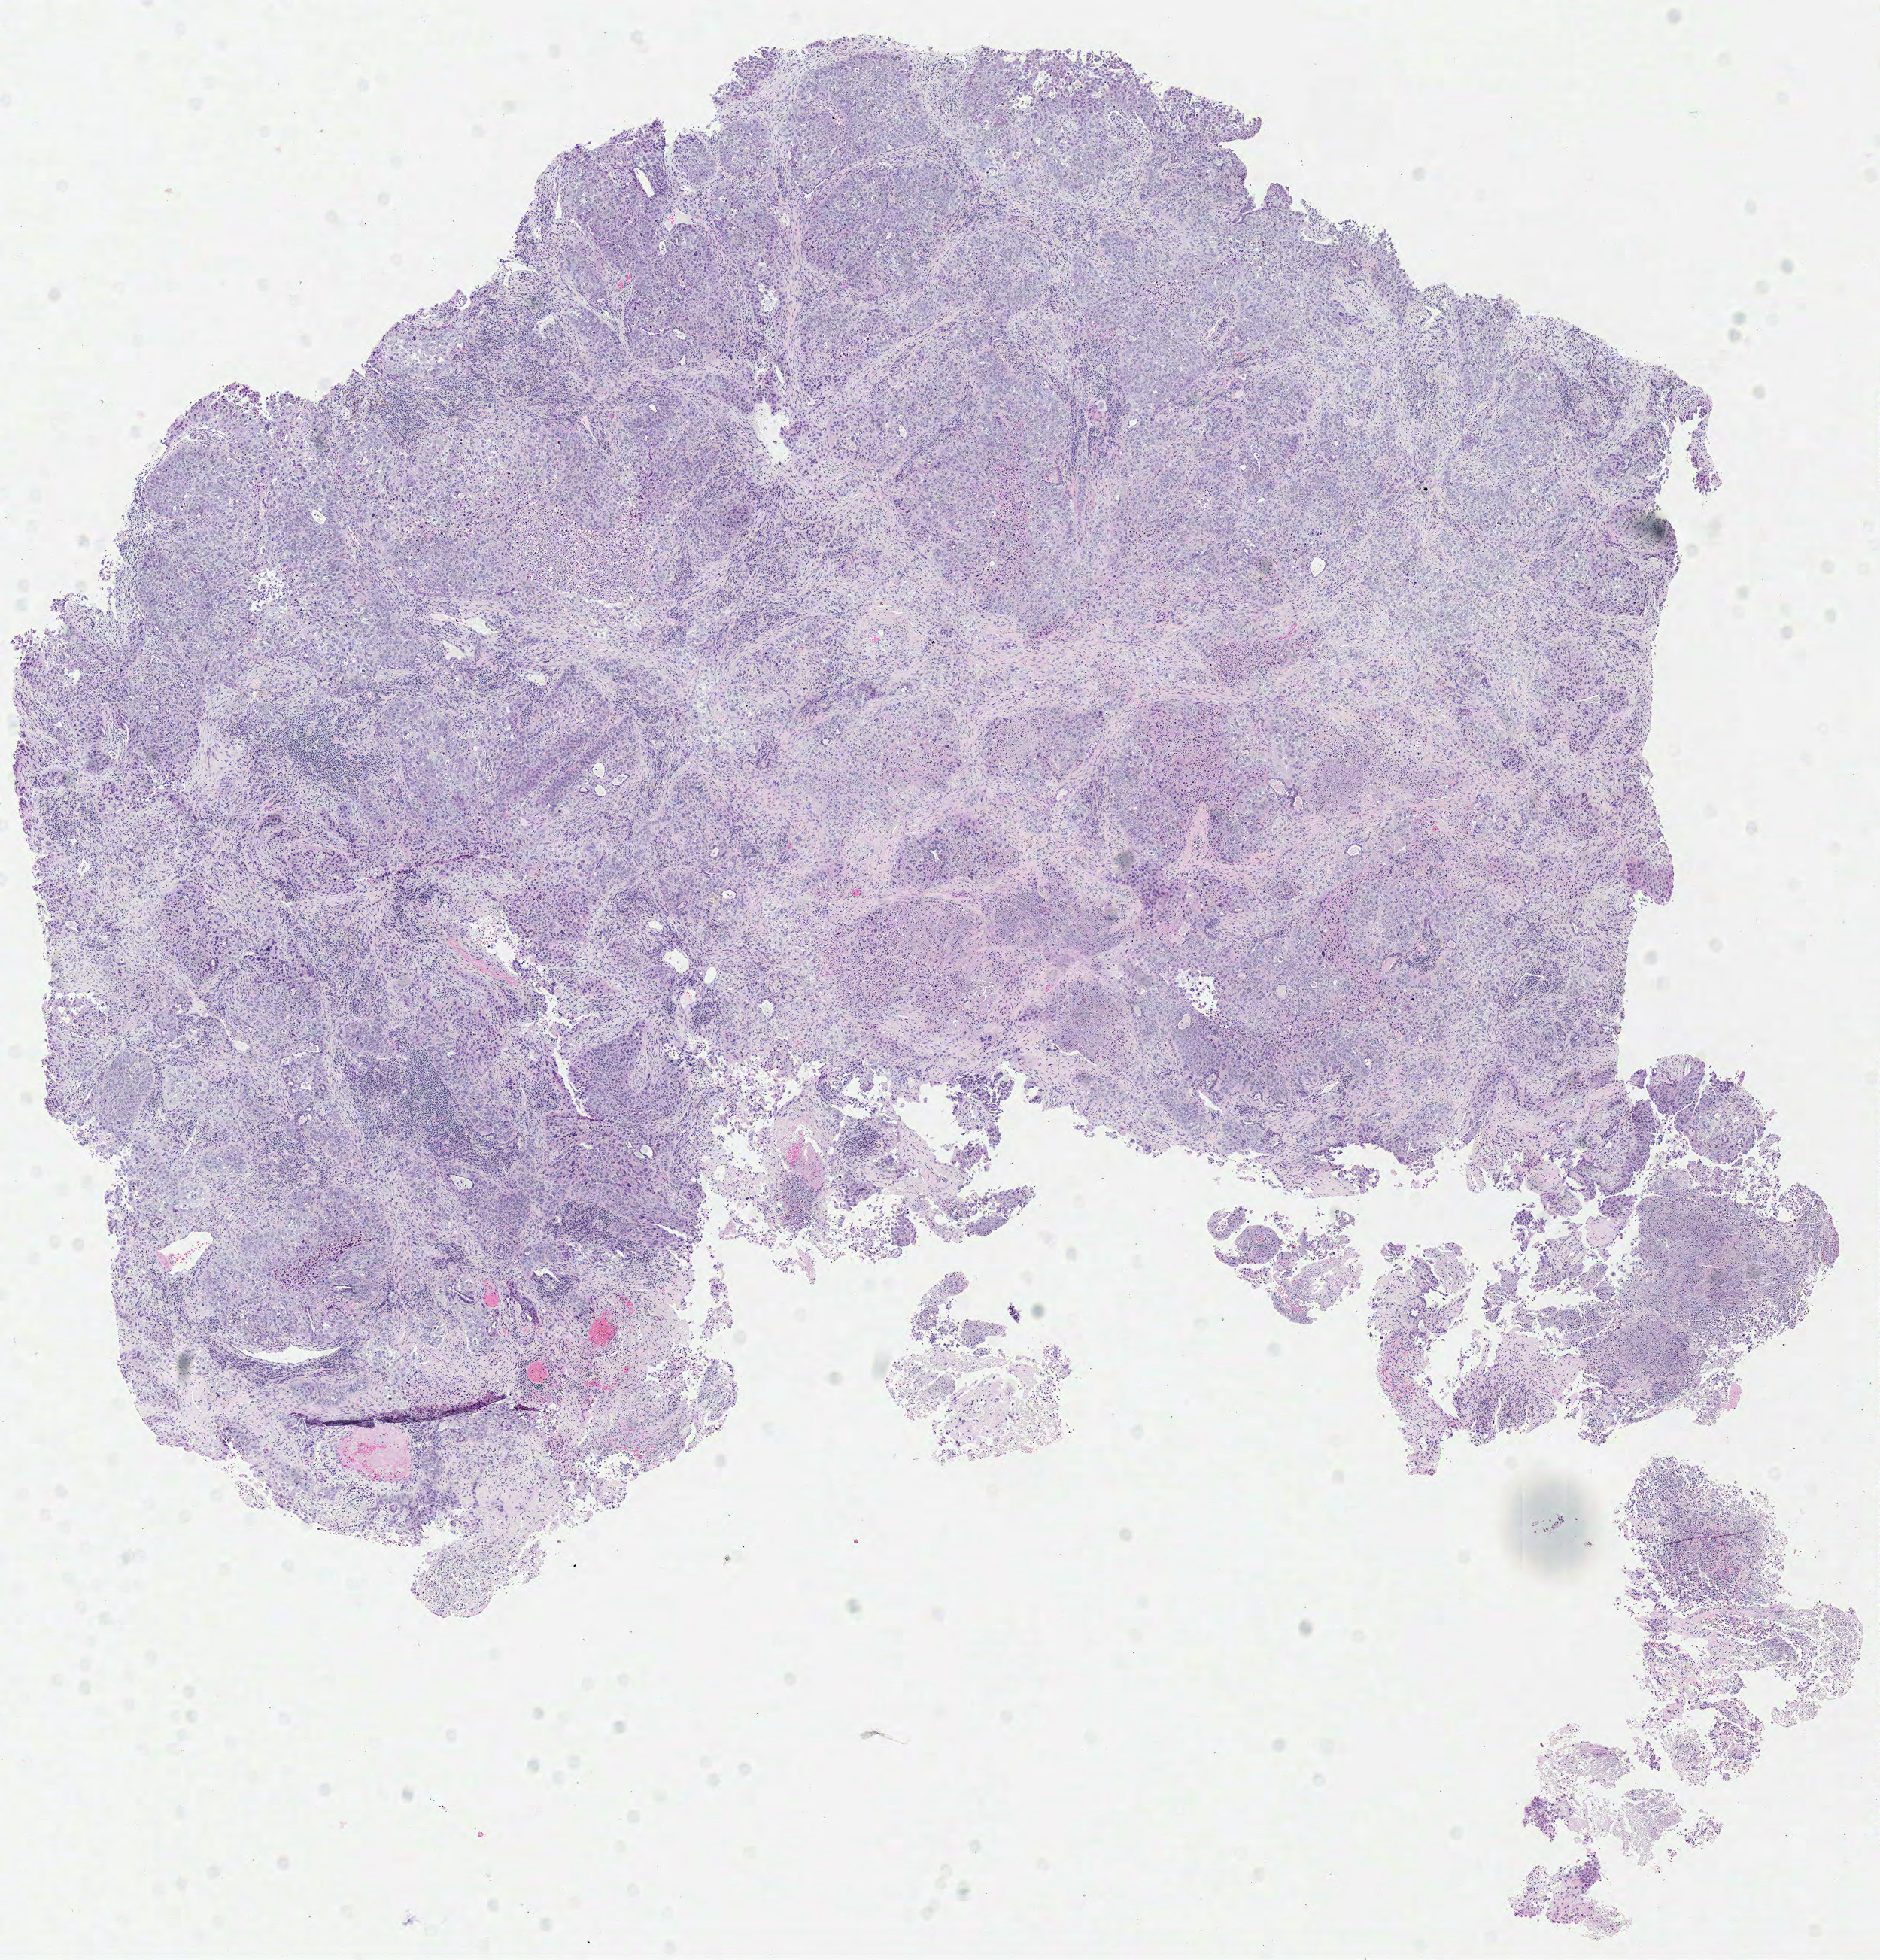
Digitized H&E tissue section (whole slide), whole scanned area (about 9.8 x 10.3 mm, acquisition: 40x scan) shown as a low-resolution overview, formalin-fixed paraffin-embedded (FFPE) diagnostic section, lung, primary tumour sample. Patient: male, age at initial diagnosis 69 years.
• diagnosis: Squamous cell carcinoma, NOS (lower lobe, lung)
• AJCC pathologic stage: IB (5th edition)